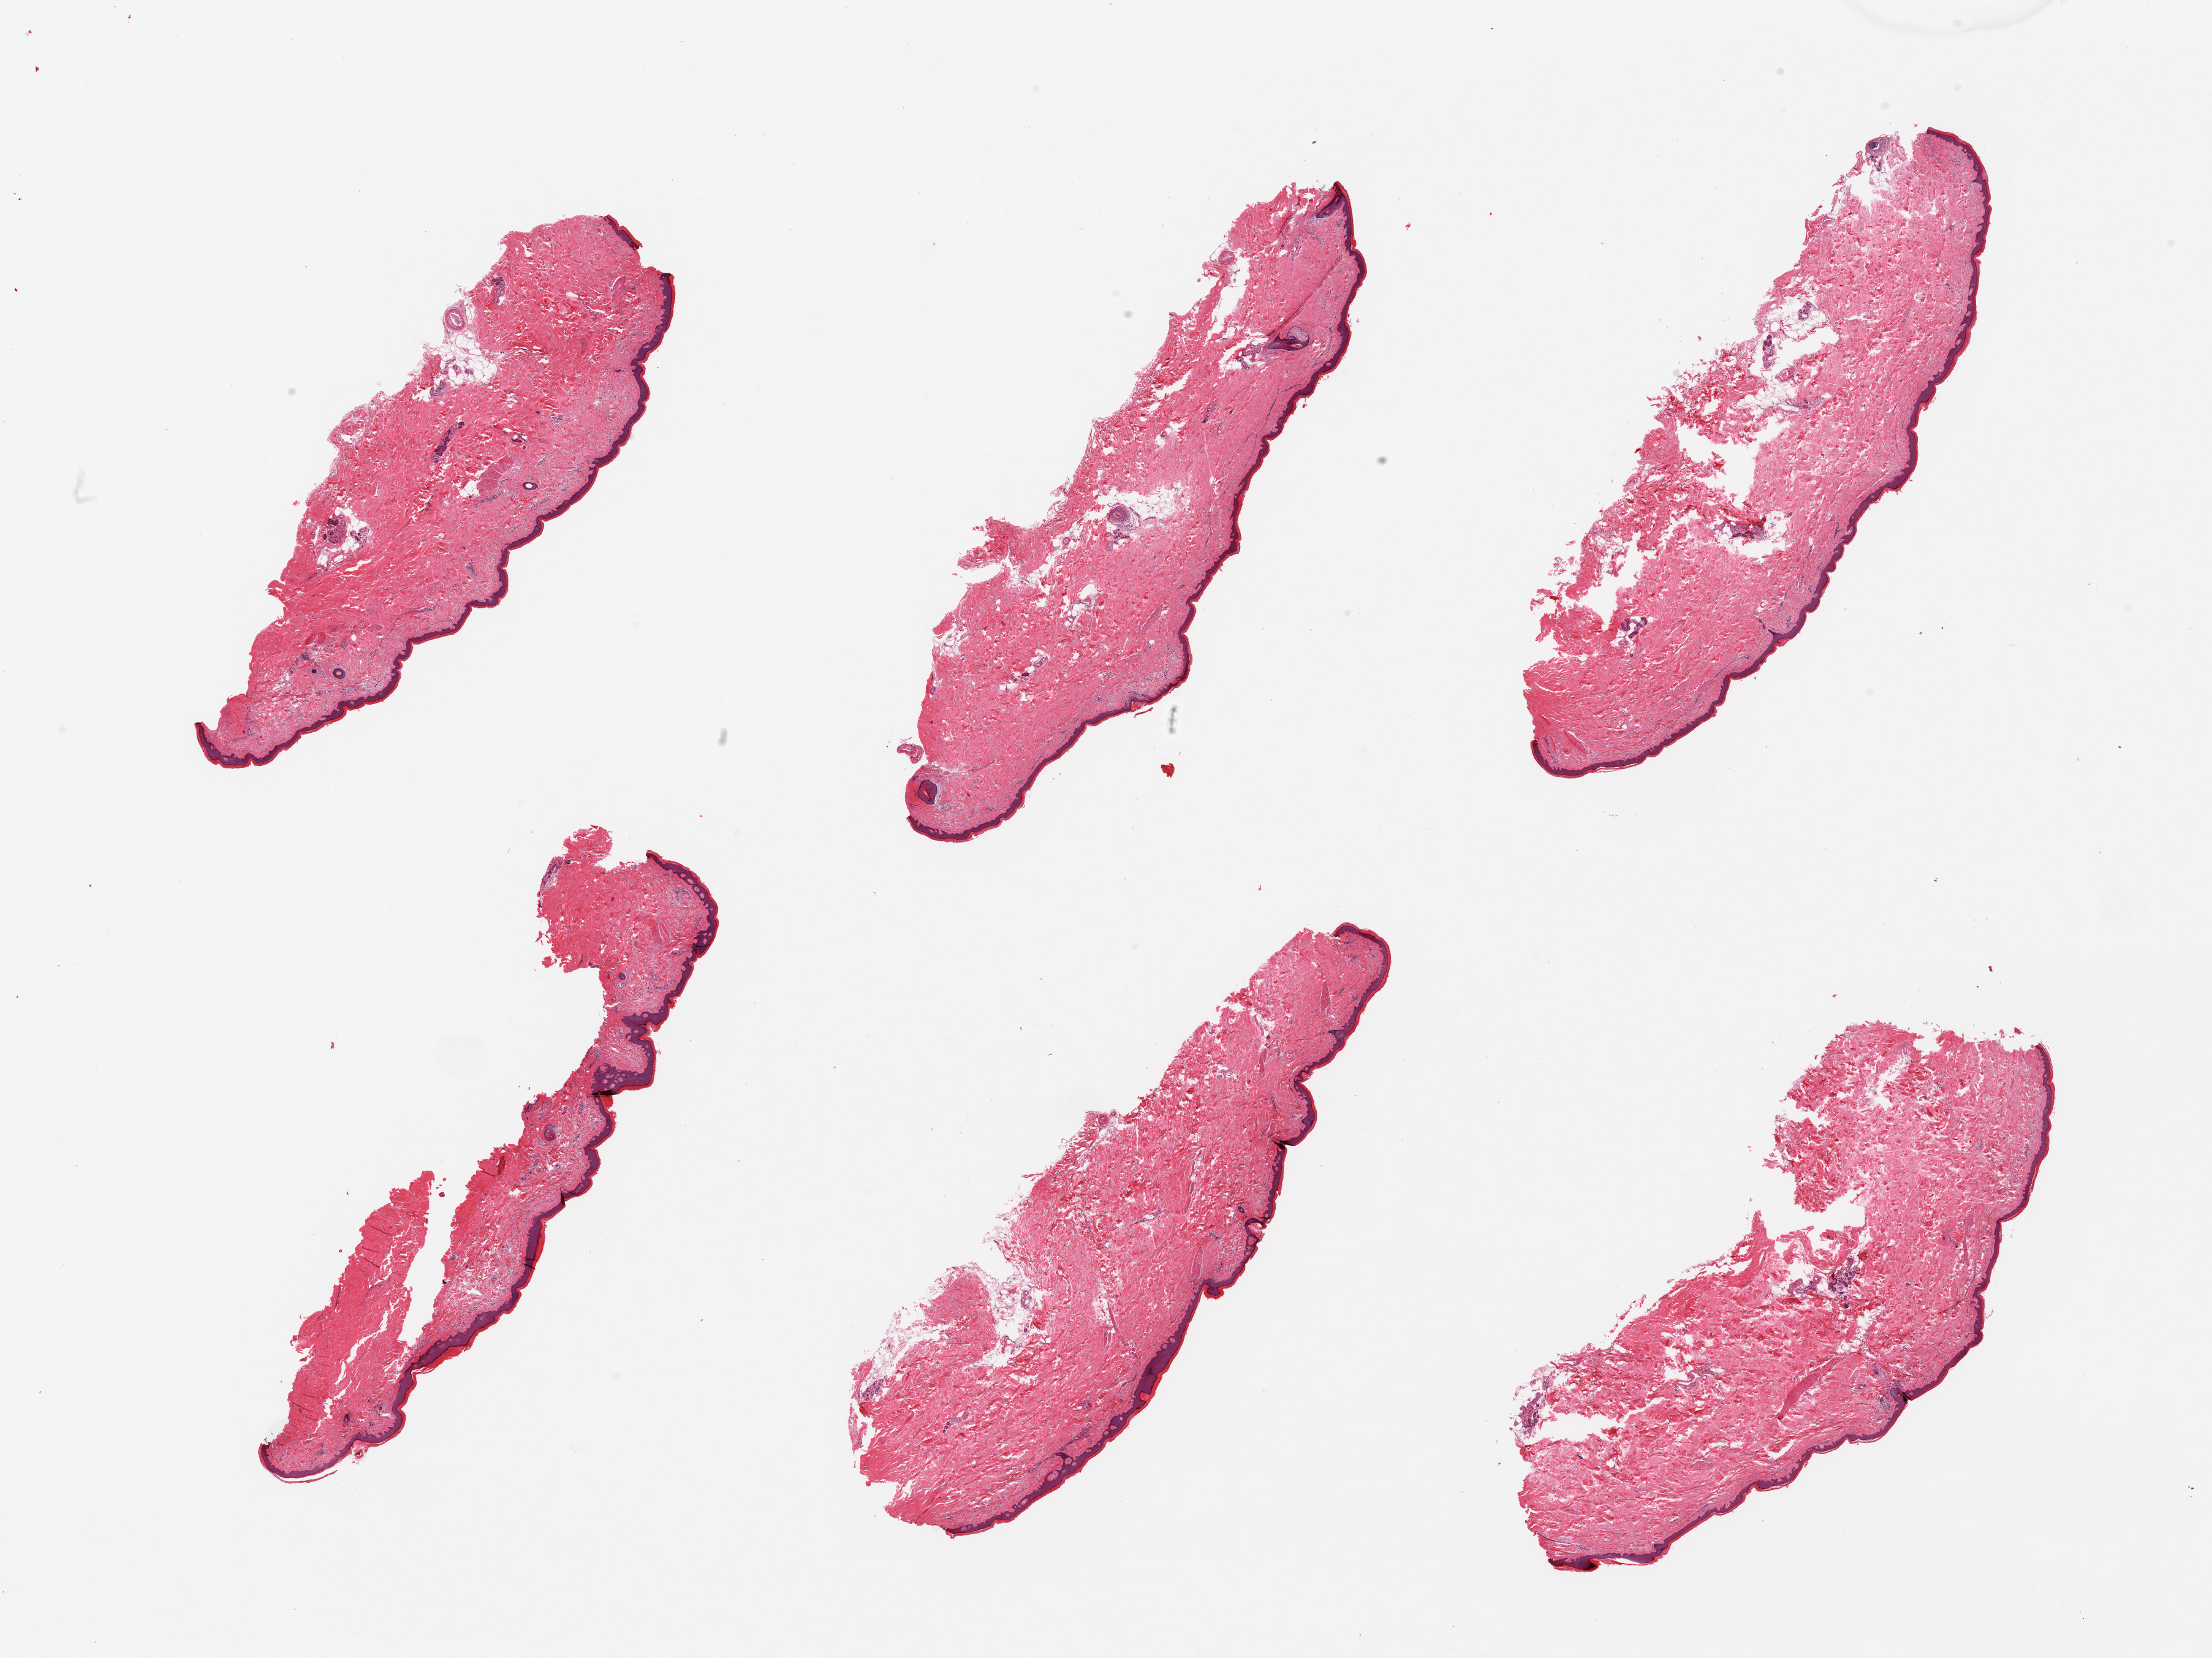
Digitized haematoxylin and eosin-stained section — low-resolution overview of the scanned area, about 28.5 x 21.4 mm (slide scanned at 20x), PAXgene-fixed, paraffin-embedded tissue, target tissue: skin of lower leg, donor tissue sample. Male donor.
Reviewer comment on this tissue sample: 6 pieces, no significant dermal fat; squamous epithelium is ~50-60 microns.